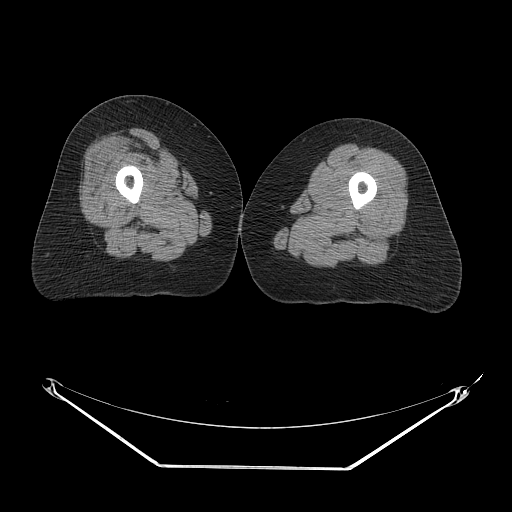
CT of an extremity soft-tissue mass (from a PET/CT study), one axial slice. Slice 17 of 267 in the series (ordered by position). 140 kVp. Soft-tissue window (W 400 / L 40 HU). 3.75 mm slice thickness. 512 × 512 image matrix, field of view 500 × 500 mm. Female patient. Case-level facts recorded for this patient, not image findings: histological type: malignant solitary fibrous tumor; grade: intermediate; site of the primary tumour: right thigh.
Outlined on this slice (expert contour drawn on MRI and transferred to this co-registered scan by the dataset authors):
- gross tumour volume including surrounding oedema: bounding box (x1, y1, x2, y2) in pixels: (126, 130, 181, 170)